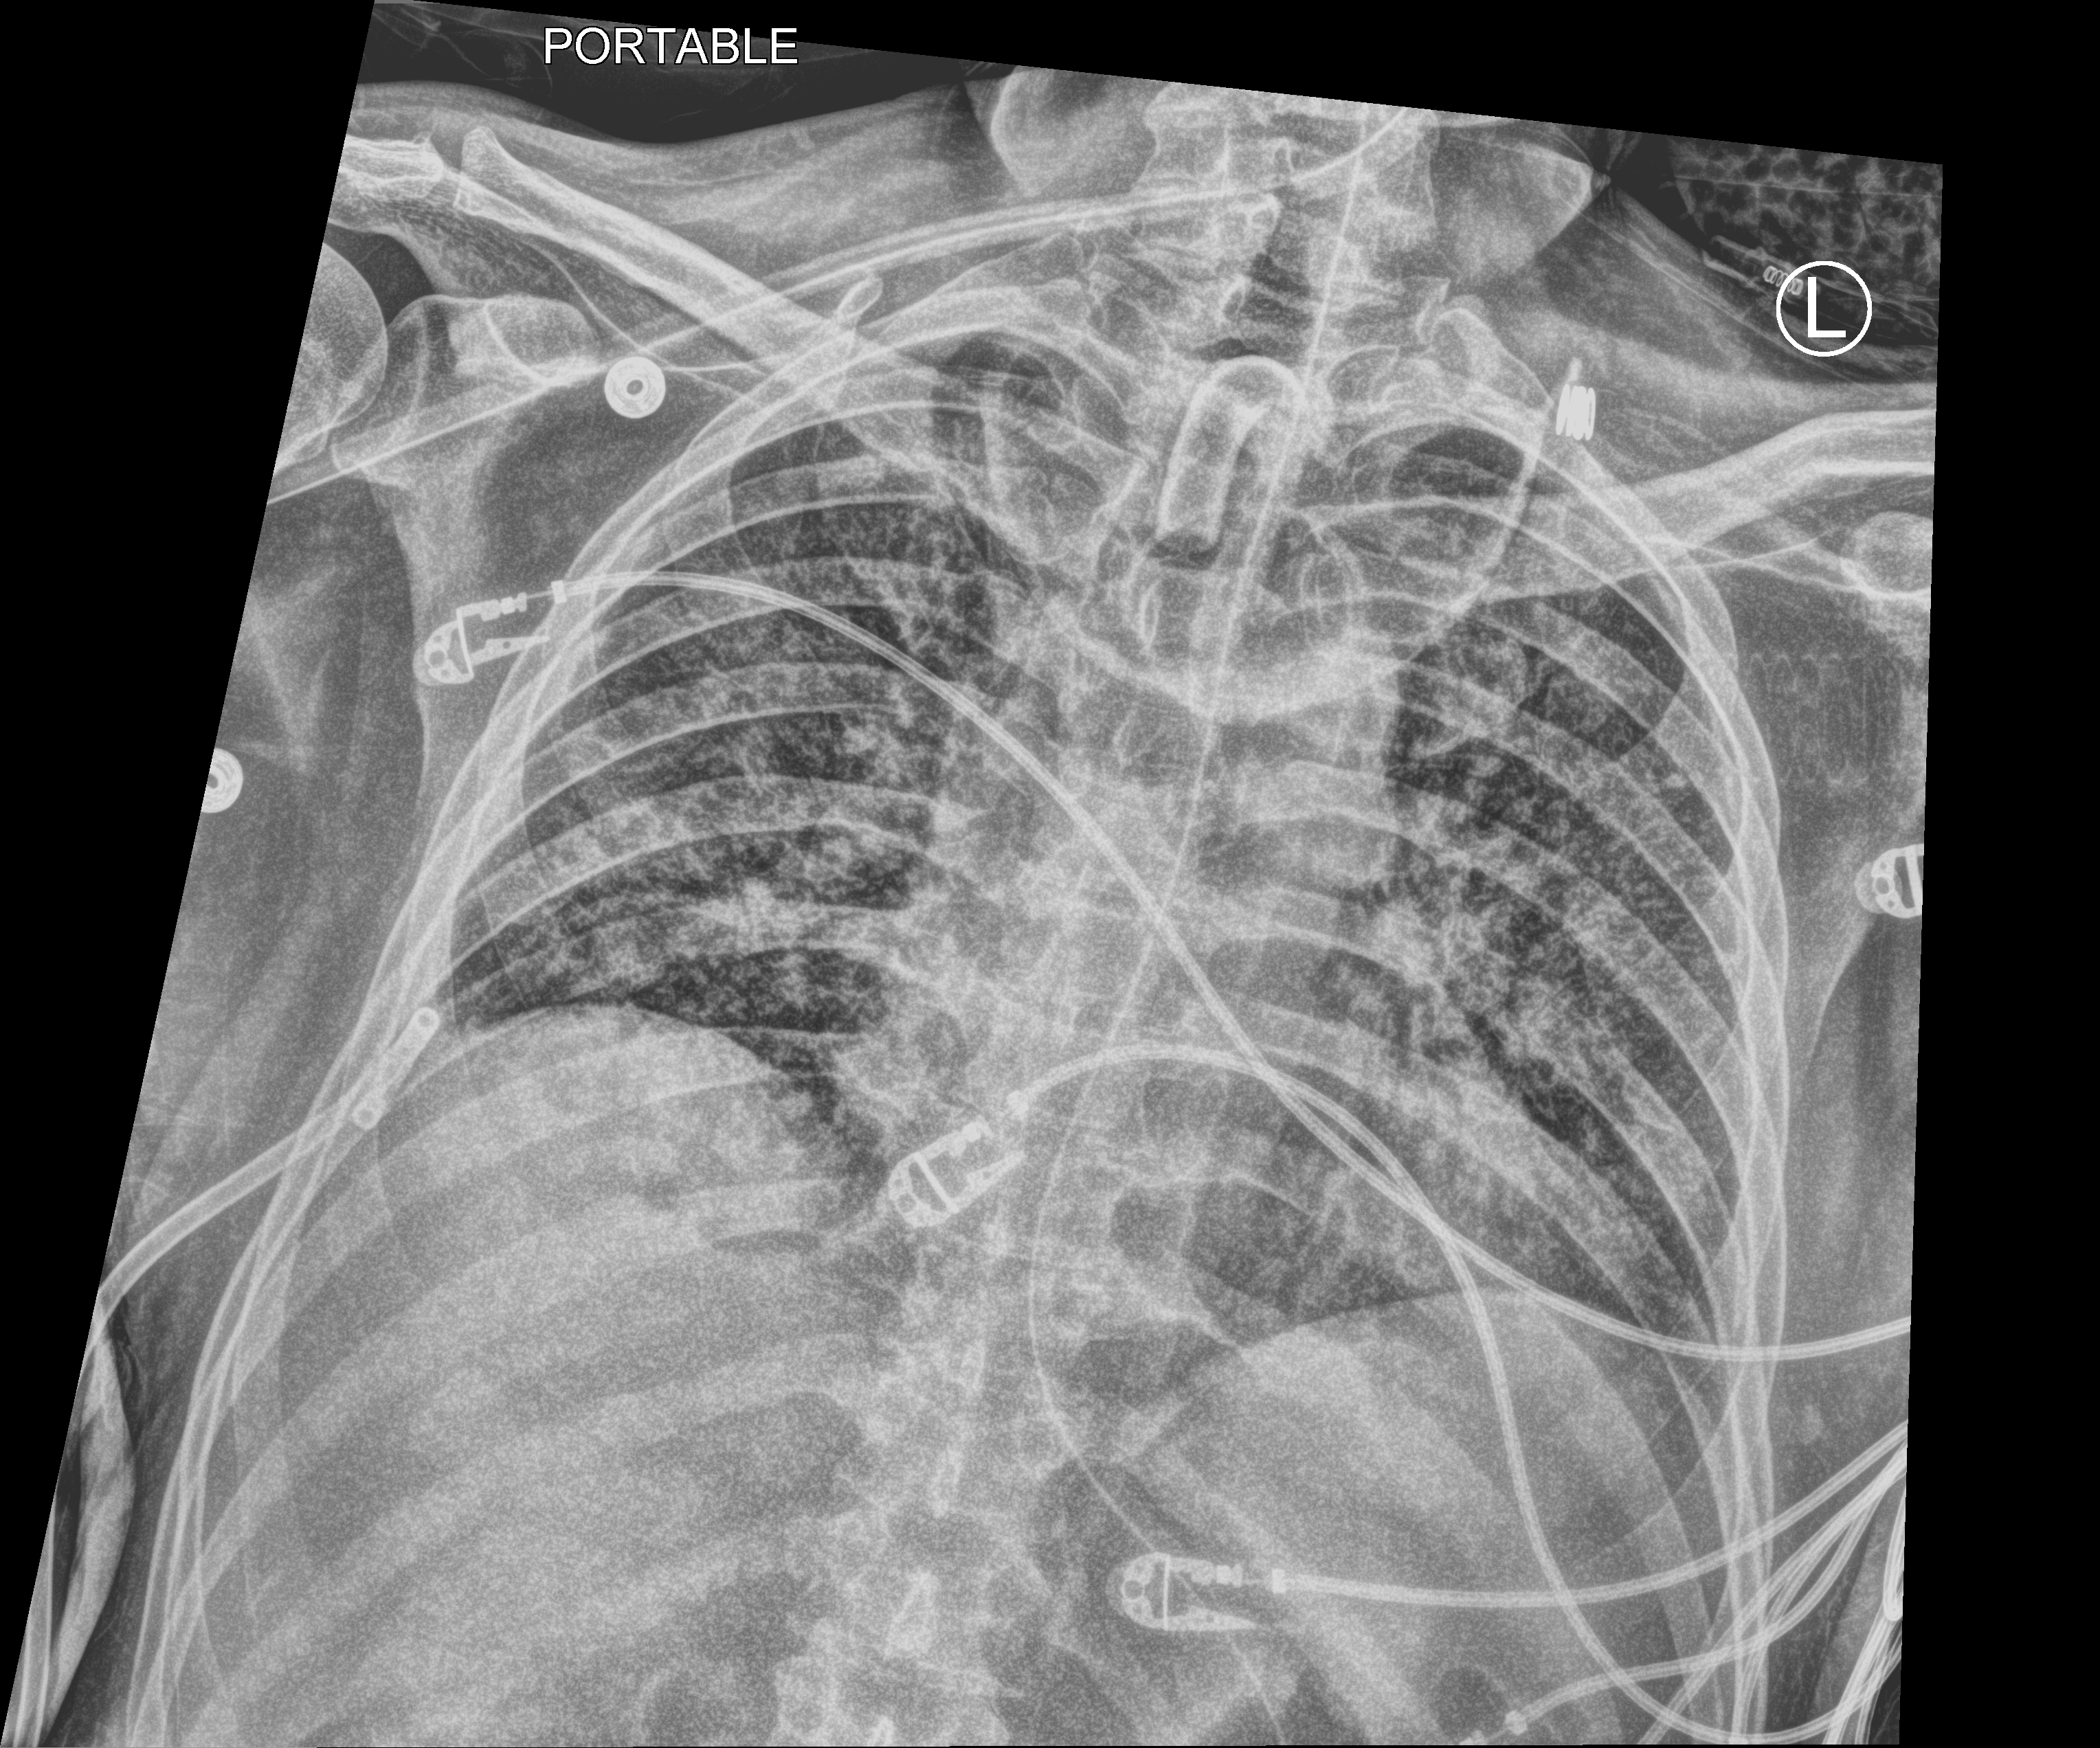
Bedside chest radiograph (computed radiography), anteroposterior (AP) projection. Patient hospitalised with COVID-19; male, aged 18–59 years.
Hospital-stay facts (about this admission, not read from this image; timing relative to this image not recorded):
- smoking status (admission record): never